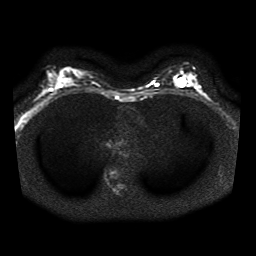
Breast MRI, one axial slice. Slice 20 of 41 in the series (ordered by position). Diffusion-weighted series; image 2 of 4 stored at this slice position (different b-values; order by instance number). 1.5 T. 5 mm slice thickness. 256 × 256 image matrix. Female patient.
Structures marked on this image (manually delineated by an expert):
- tumour on diffusion-weighted imaging: bounding box [x1, y1, x2, y2] px = [187, 78, 194, 85]